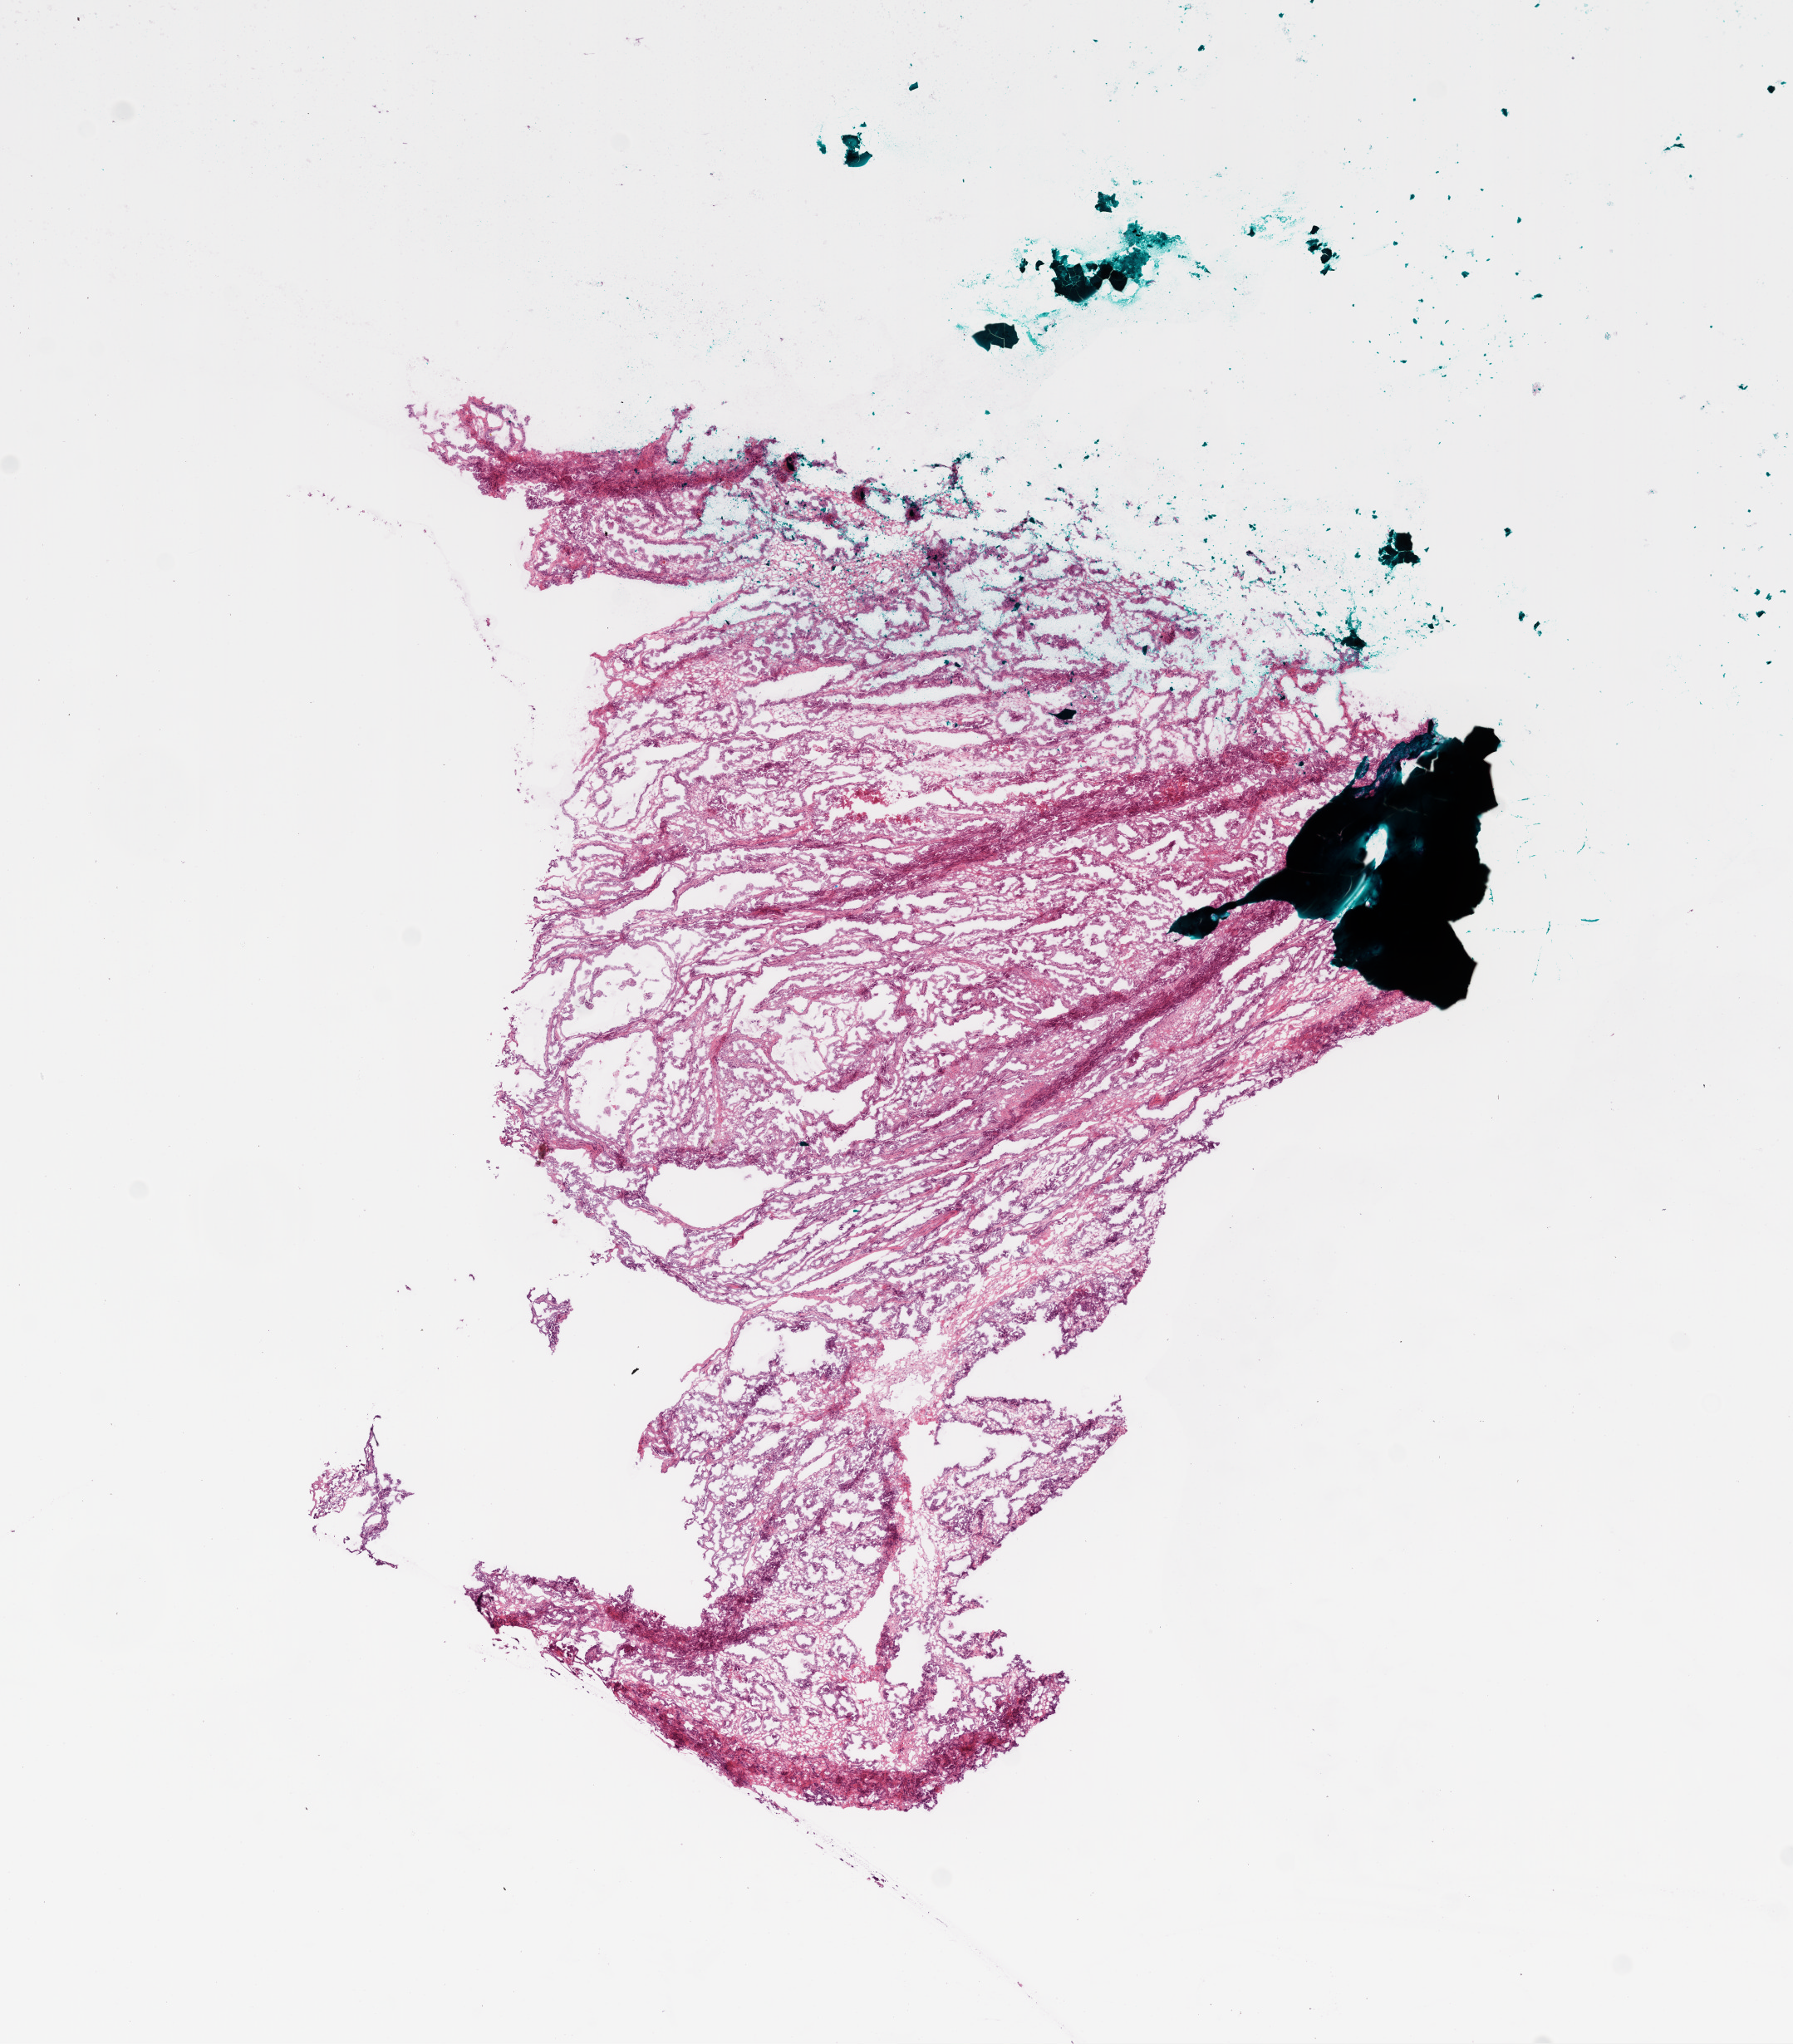
Digitized Hematoxylin and eosin (H&E) stained tissue section (whole slide) — whole scanned area (about 8.7 x 9.9 mm) shown as a low-resolution overview, frozen section, primary tumour sample from the ovary. Patient: female, age at initial diagnosis 52 years. Histologic grade: G3 (poorly differentiated). Composition of this section per pathologist review: tumour cells 90%, tumour nuclei 90%, normal cells 5%, stromal cells 5%, necrosis 0%.
Diagnosis: Serous cystadenocarcinoma, NOS. FIGO stage: IV.